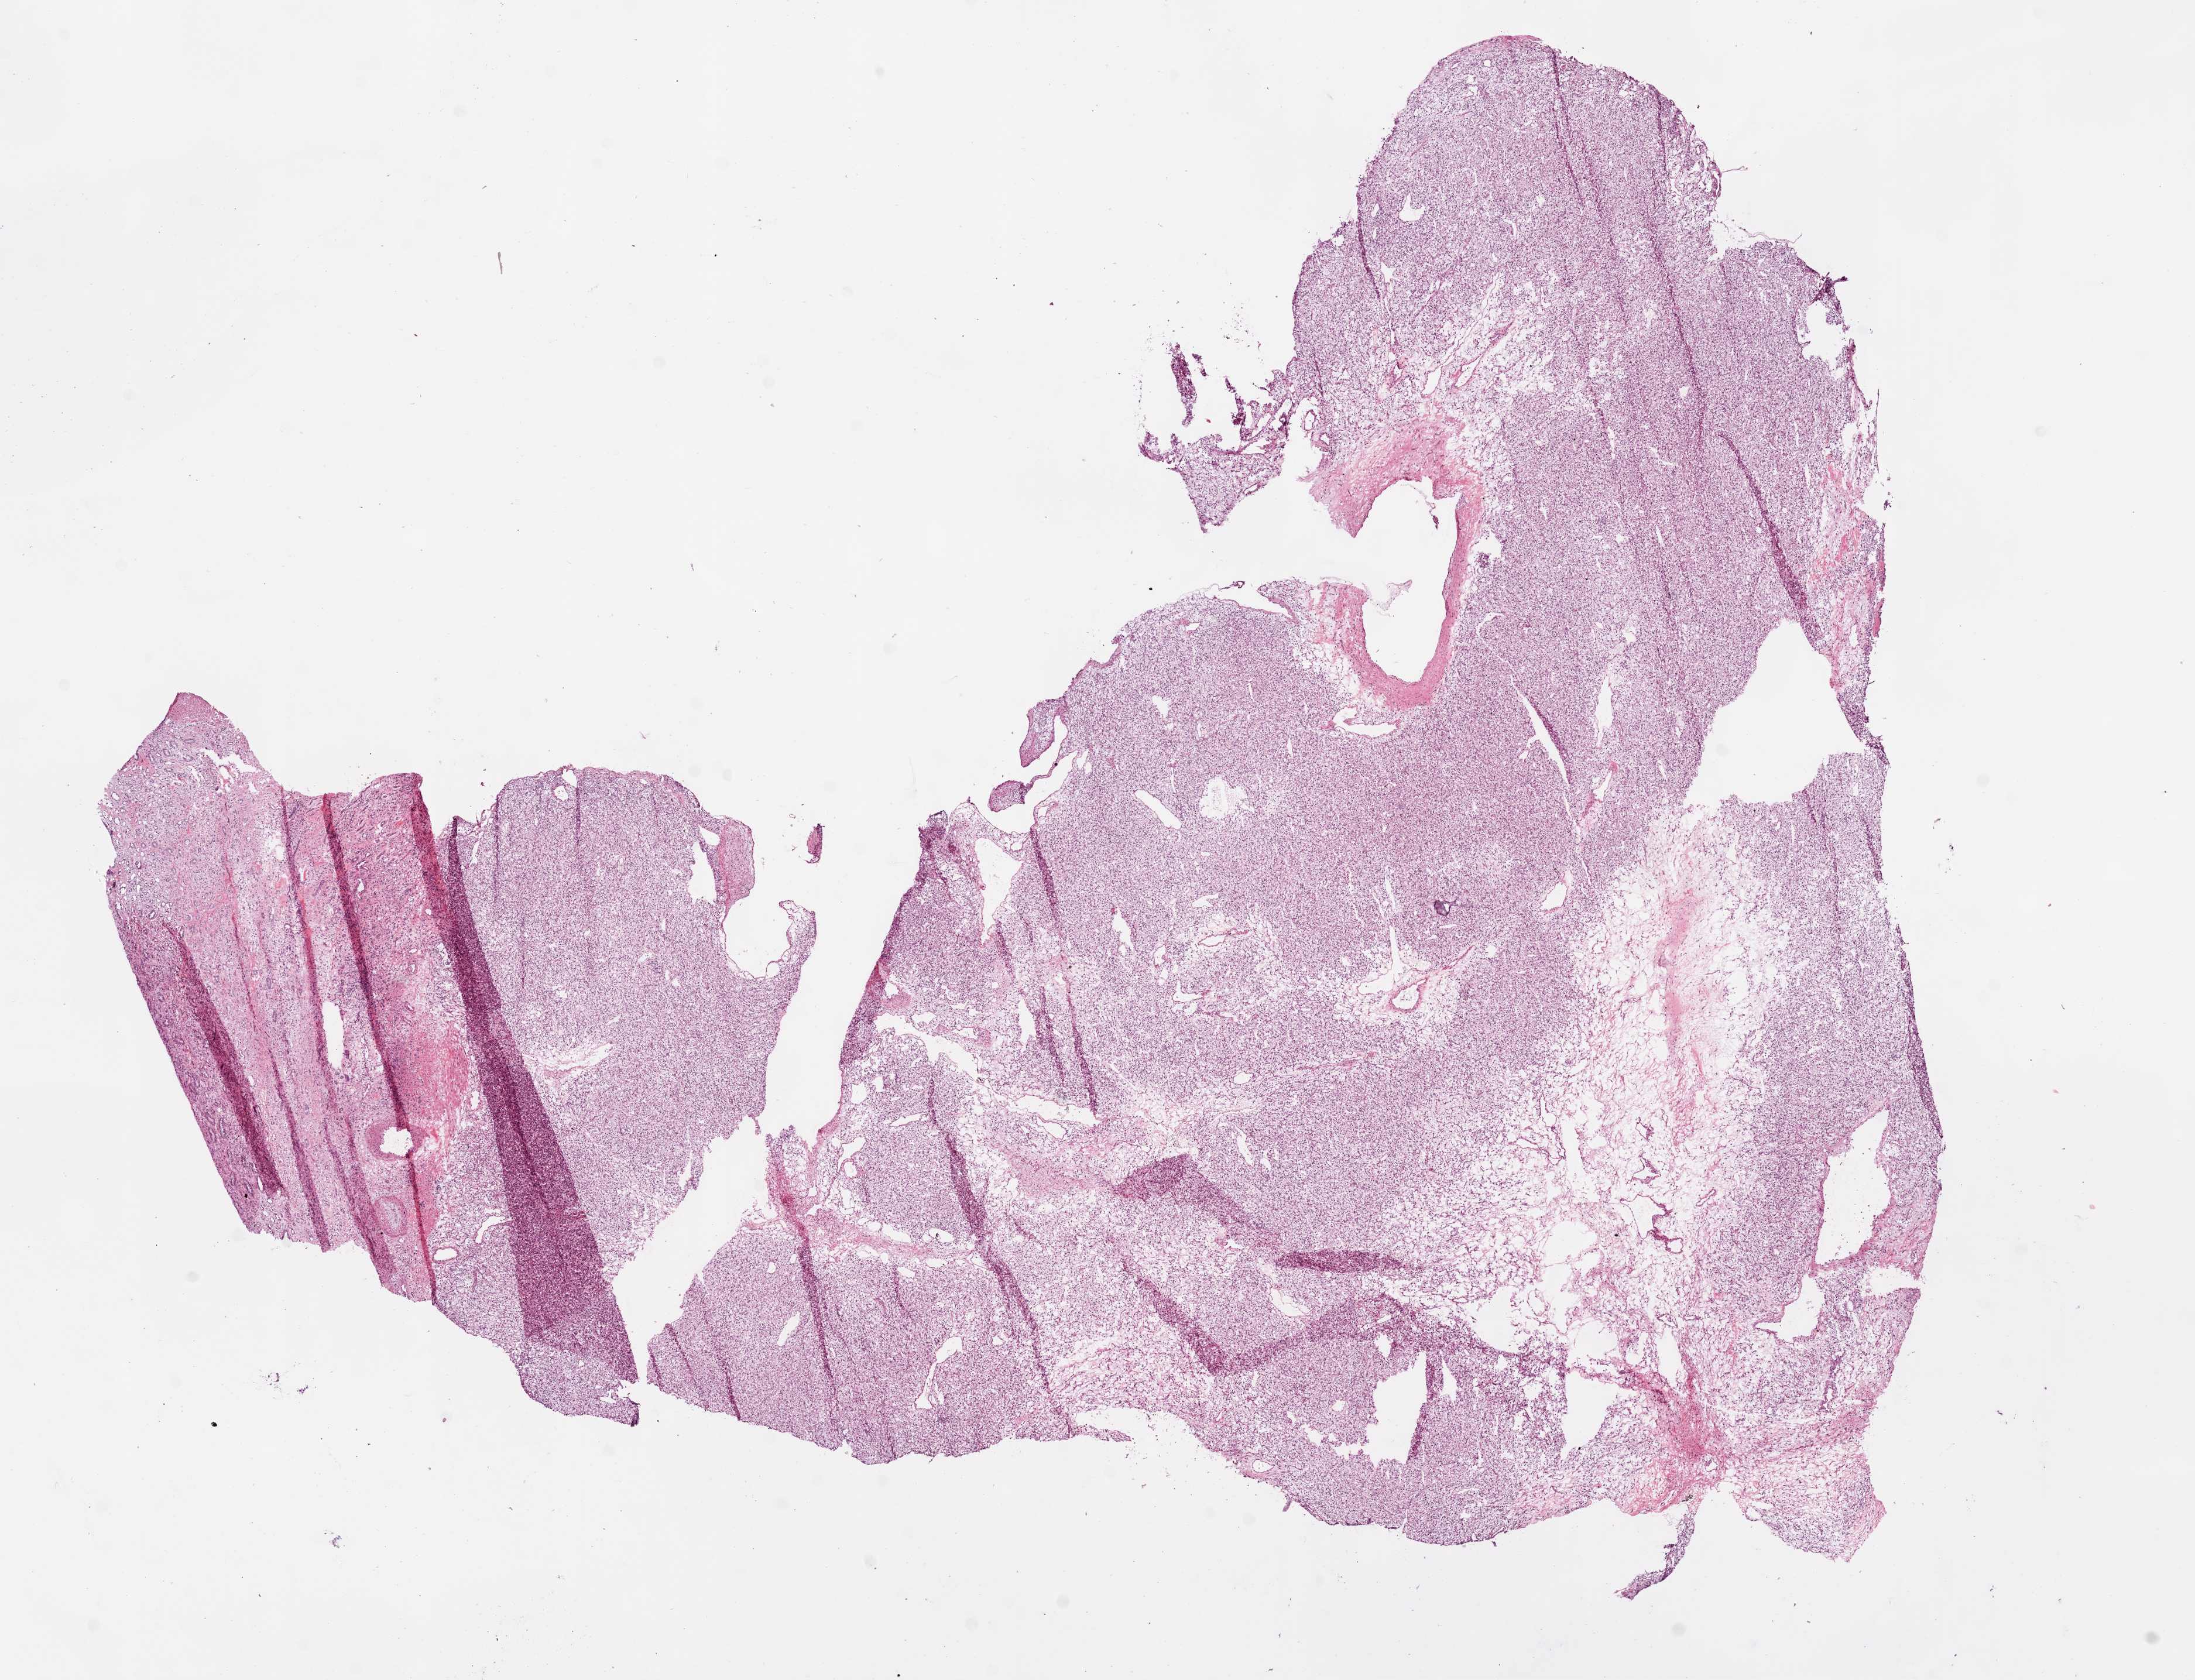
Whole-slide histology image, Hematoxylin and eosin (H&E) stained, low-resolution overview of the scanned area, about 15.0 x 11.5 mm, frozen section from the bottom of the tissue portion, sample: primary tumour, kidney. Male, age 42 years at initial diagnosis. Histologic grade: G3 (poorly differentiated). Pathologist review of this section (percent, as recorded): tumour cells 70%, tumour nuclei 80%, normal cells 15%, stromal cells 15%, necrosis 0%.
Laterality: left. Histologic diagnosis: Clear cell adenocarcinoma, NOS. AJCC pathologic stage: I. TNM: T1b NX M0.